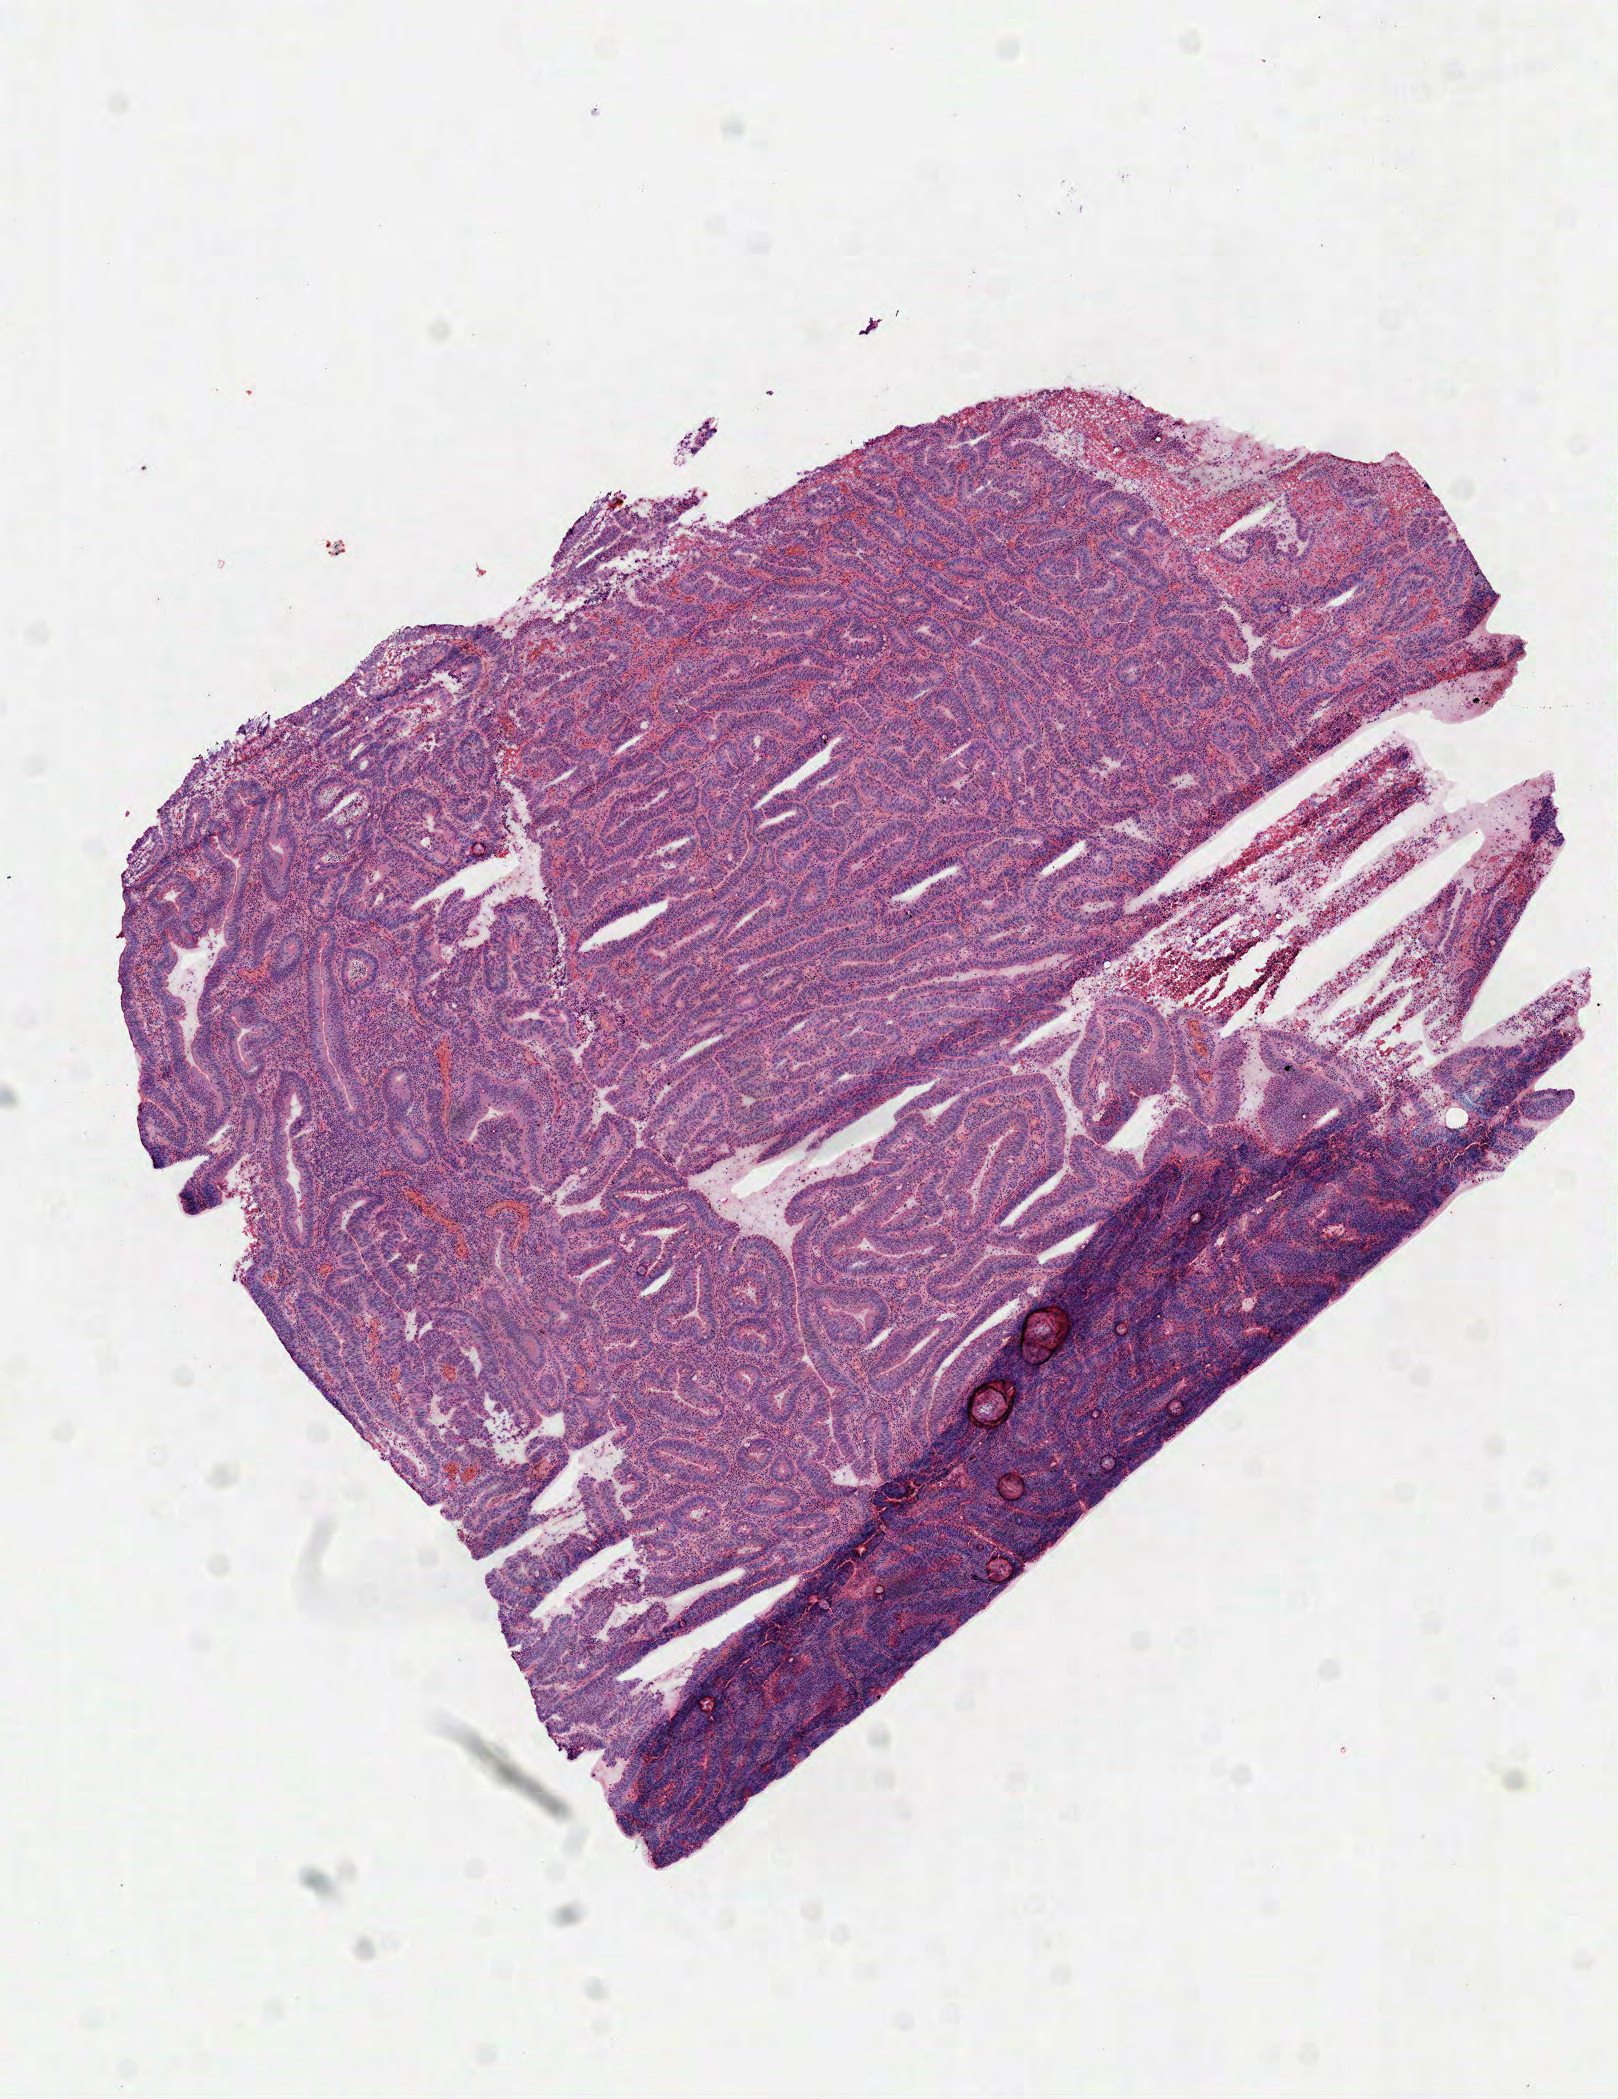
Hematoxylin and eosin (H&E) stained whole-slide image, whole scanned area (about 6.5 x 8.5 mm) shown as a low-resolution overview, frozen section from the top of the tissue portion, primary tumour sample from the rectum. Patient: female, age at initial diagnosis 77 years. Pathologist review of this section (percent, as recorded): tumour cells 60%, tumour nuclei 75%, normal cells 15%, stromal cells 10%, necrosis 15%.
• diagnosis: Adenocarcinoma in tubulovillous adenoma